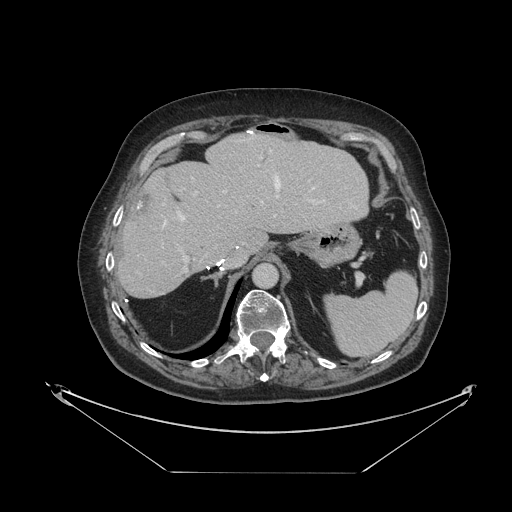
Contrast-enhanced abdominal CT, one axial slice. Position 76 of 121 along the scan axis. 120 kVp. Intravenous contrast given. Soft-tissue window (W 400 / L 40 HU). 2.5 mm slice thickness. 512 × 512 image matrix, field of view 500 × 500 mm. Male patient, age 68 years. From the clinical record (not read from this slice): diagnosis: colorectal cancer liver metastases, imaged before liver resection; multiple liver metastases: no; largest metastasis: 4 cm; disease in both lobes: no.
Structures marked on this image (outlined manually by an expert reader):
- hepatic veins: bounding box [x1, y1, x2, y2] px = [162, 150, 315, 230]
- liver: [119, 134, 369, 298]
- planned liver remnant (the part of the liver to remain after resection): [119, 135, 369, 297]
- portal vein (with intrahepatic branches): [183, 164, 315, 272]
- liver metastasis: [136, 192, 152, 215]